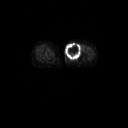
FDG PET of an extremity soft-tissue mass (from a PET/CT study), one axial slice; slice 34 of 91 in the series (ordered by position); 3.27 mm slice thickness; 128 × 128 image matrix, field of view 700 × 700 mm. Female patient, age 74 years. From the clinical record (not read from this slice): histological type: pleomorphic leiomyosarcoma; grade: high; site of the primary tumour: left thigh.
Annotated regions visible in this slice (expert contour drawn on MRI and transferred to this co-registered scan by the dataset authors):
- gross tumour volume including surrounding oedema: bounding box [x1, y1, x2, y2] px = [65, 42, 82, 60]
- gross tumour volume (mass): [65, 42, 82, 60]